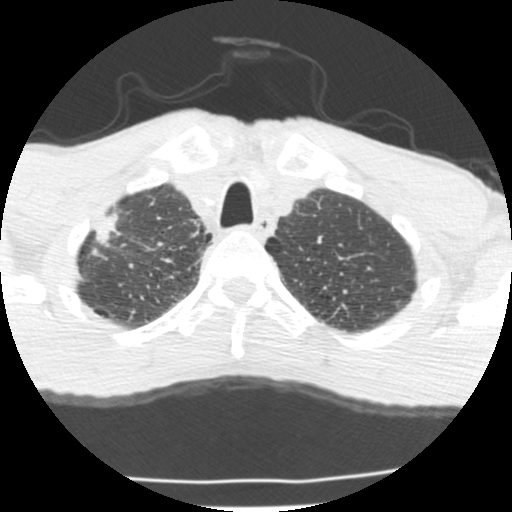
Low-dose screening chest CT, axial slice. Second screening round (one year after baseline). Lung window (W 1500 / L -600 HU). 2.5 mm slice thickness. Slice 31 of 214 in the series. 512 × 512 image matrix. Male, age 62 years at enrolment.
- Expert-annotated lung lesion, bounding box [x1, y1, x2, y2] px = [69, 213, 139, 273].
- Screening reader's record for this exam (one nodule recorded; not confirmed to be the boxed lesion): non-calcified nodule or mass ≥4 mm, right upper lobe, 23 × 11 mm, spiculated (stellate) margins, soft tissue attenuation, pre-existing on the prior screen: yes.